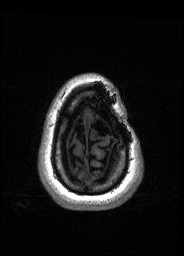
Pre-operative brain MRI before brain-tumour surgery, one axial slice. Slice 29 of 176 in the series (ordered by position). T1-weighted post-contrast. 184 × 256 image matrix, field of view 180 × 250 mm. Case-level facts recorded for this patient, not image findings: histopathology: Oligodendroglioma; WHO grade: 2.
Outlined on this slice (outlined manually by an expert reader):
- tumour: bounding box [x1, y1, x2, y2] px = [90, 112, 99, 124]